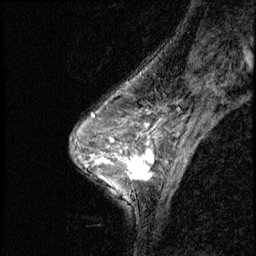
Breast MRI (dynamic contrast-enhanced), one sagittal slice; position 35 of 56 along the scan axis; dynamic contrast-enhanced series, image 2 of 3 at this slice position (ordered by acquisition); 1.5 T; TE 4.2 ms, TR 8.7 ms; 2.5 mm slice thickness; 256 × 256 image matrix, field of view 180 × 180 mm. Female patient, age 50 years. From the clinical record (not read from this slice): setting: breast cancer imaged before/during neoadjuvant chemotherapy; receptor status: HR-positive, HER2-negative.
Annotated regions visible in this slice (semi-automatic segmentation, software-assisted and operator-edited):
- analysis volume of interest (the breast-tissue region the enhancement analysis was run in; not a lesion): bounding box (x1, y1, x2, y2) in pixels: (119, 136, 169, 190)
- tumour enhancement mask (voxels above the 140 % enhancement threshold inside the analysis volume of interest): (119, 149, 154, 181)